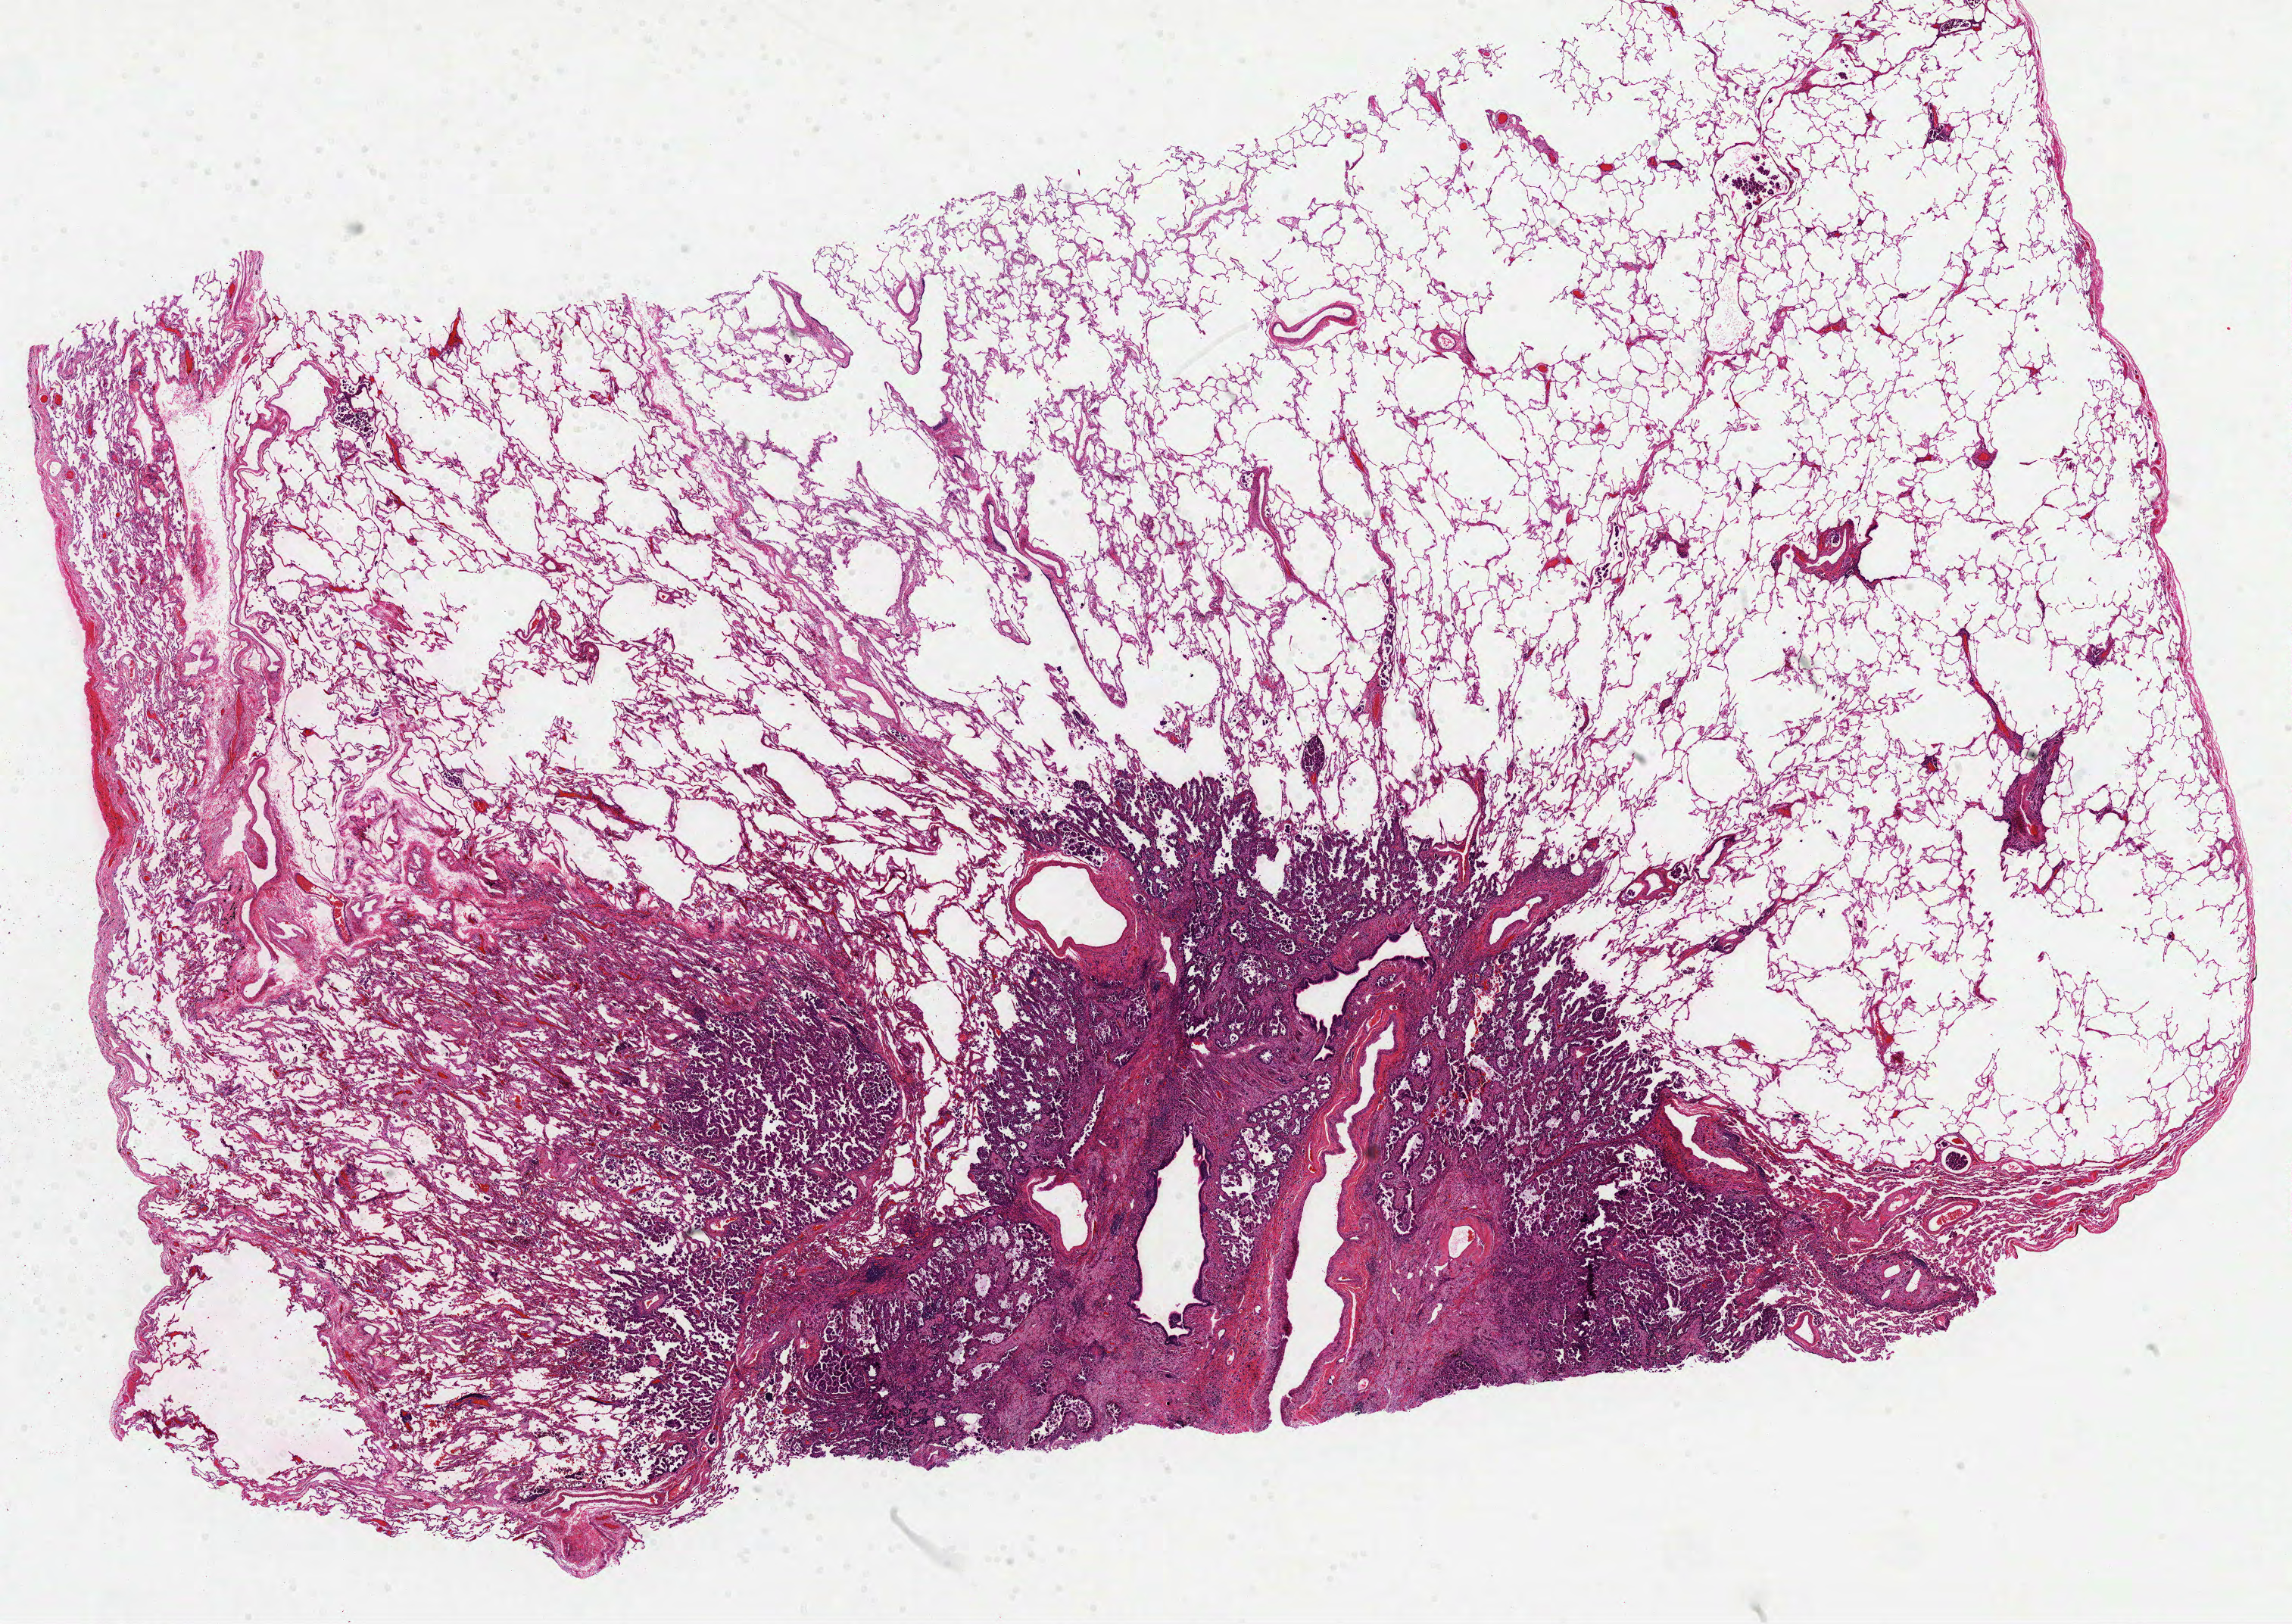
Digitized Hematoxylin and eosin (H&E) stained tissue section (whole slide) — a low-resolution overview of the entire scanned area, about 24.4 x 17.3 mm (from a 40x scan). Formalin-fixed paraffin-embedded (FFPE) diagnostic section. Lung, primary tumour sample. Patient: female, age at initial diagnosis 69 years.
Pathologic diagnosis: Adenocarcinoma, NOS (middle lobe, lung).